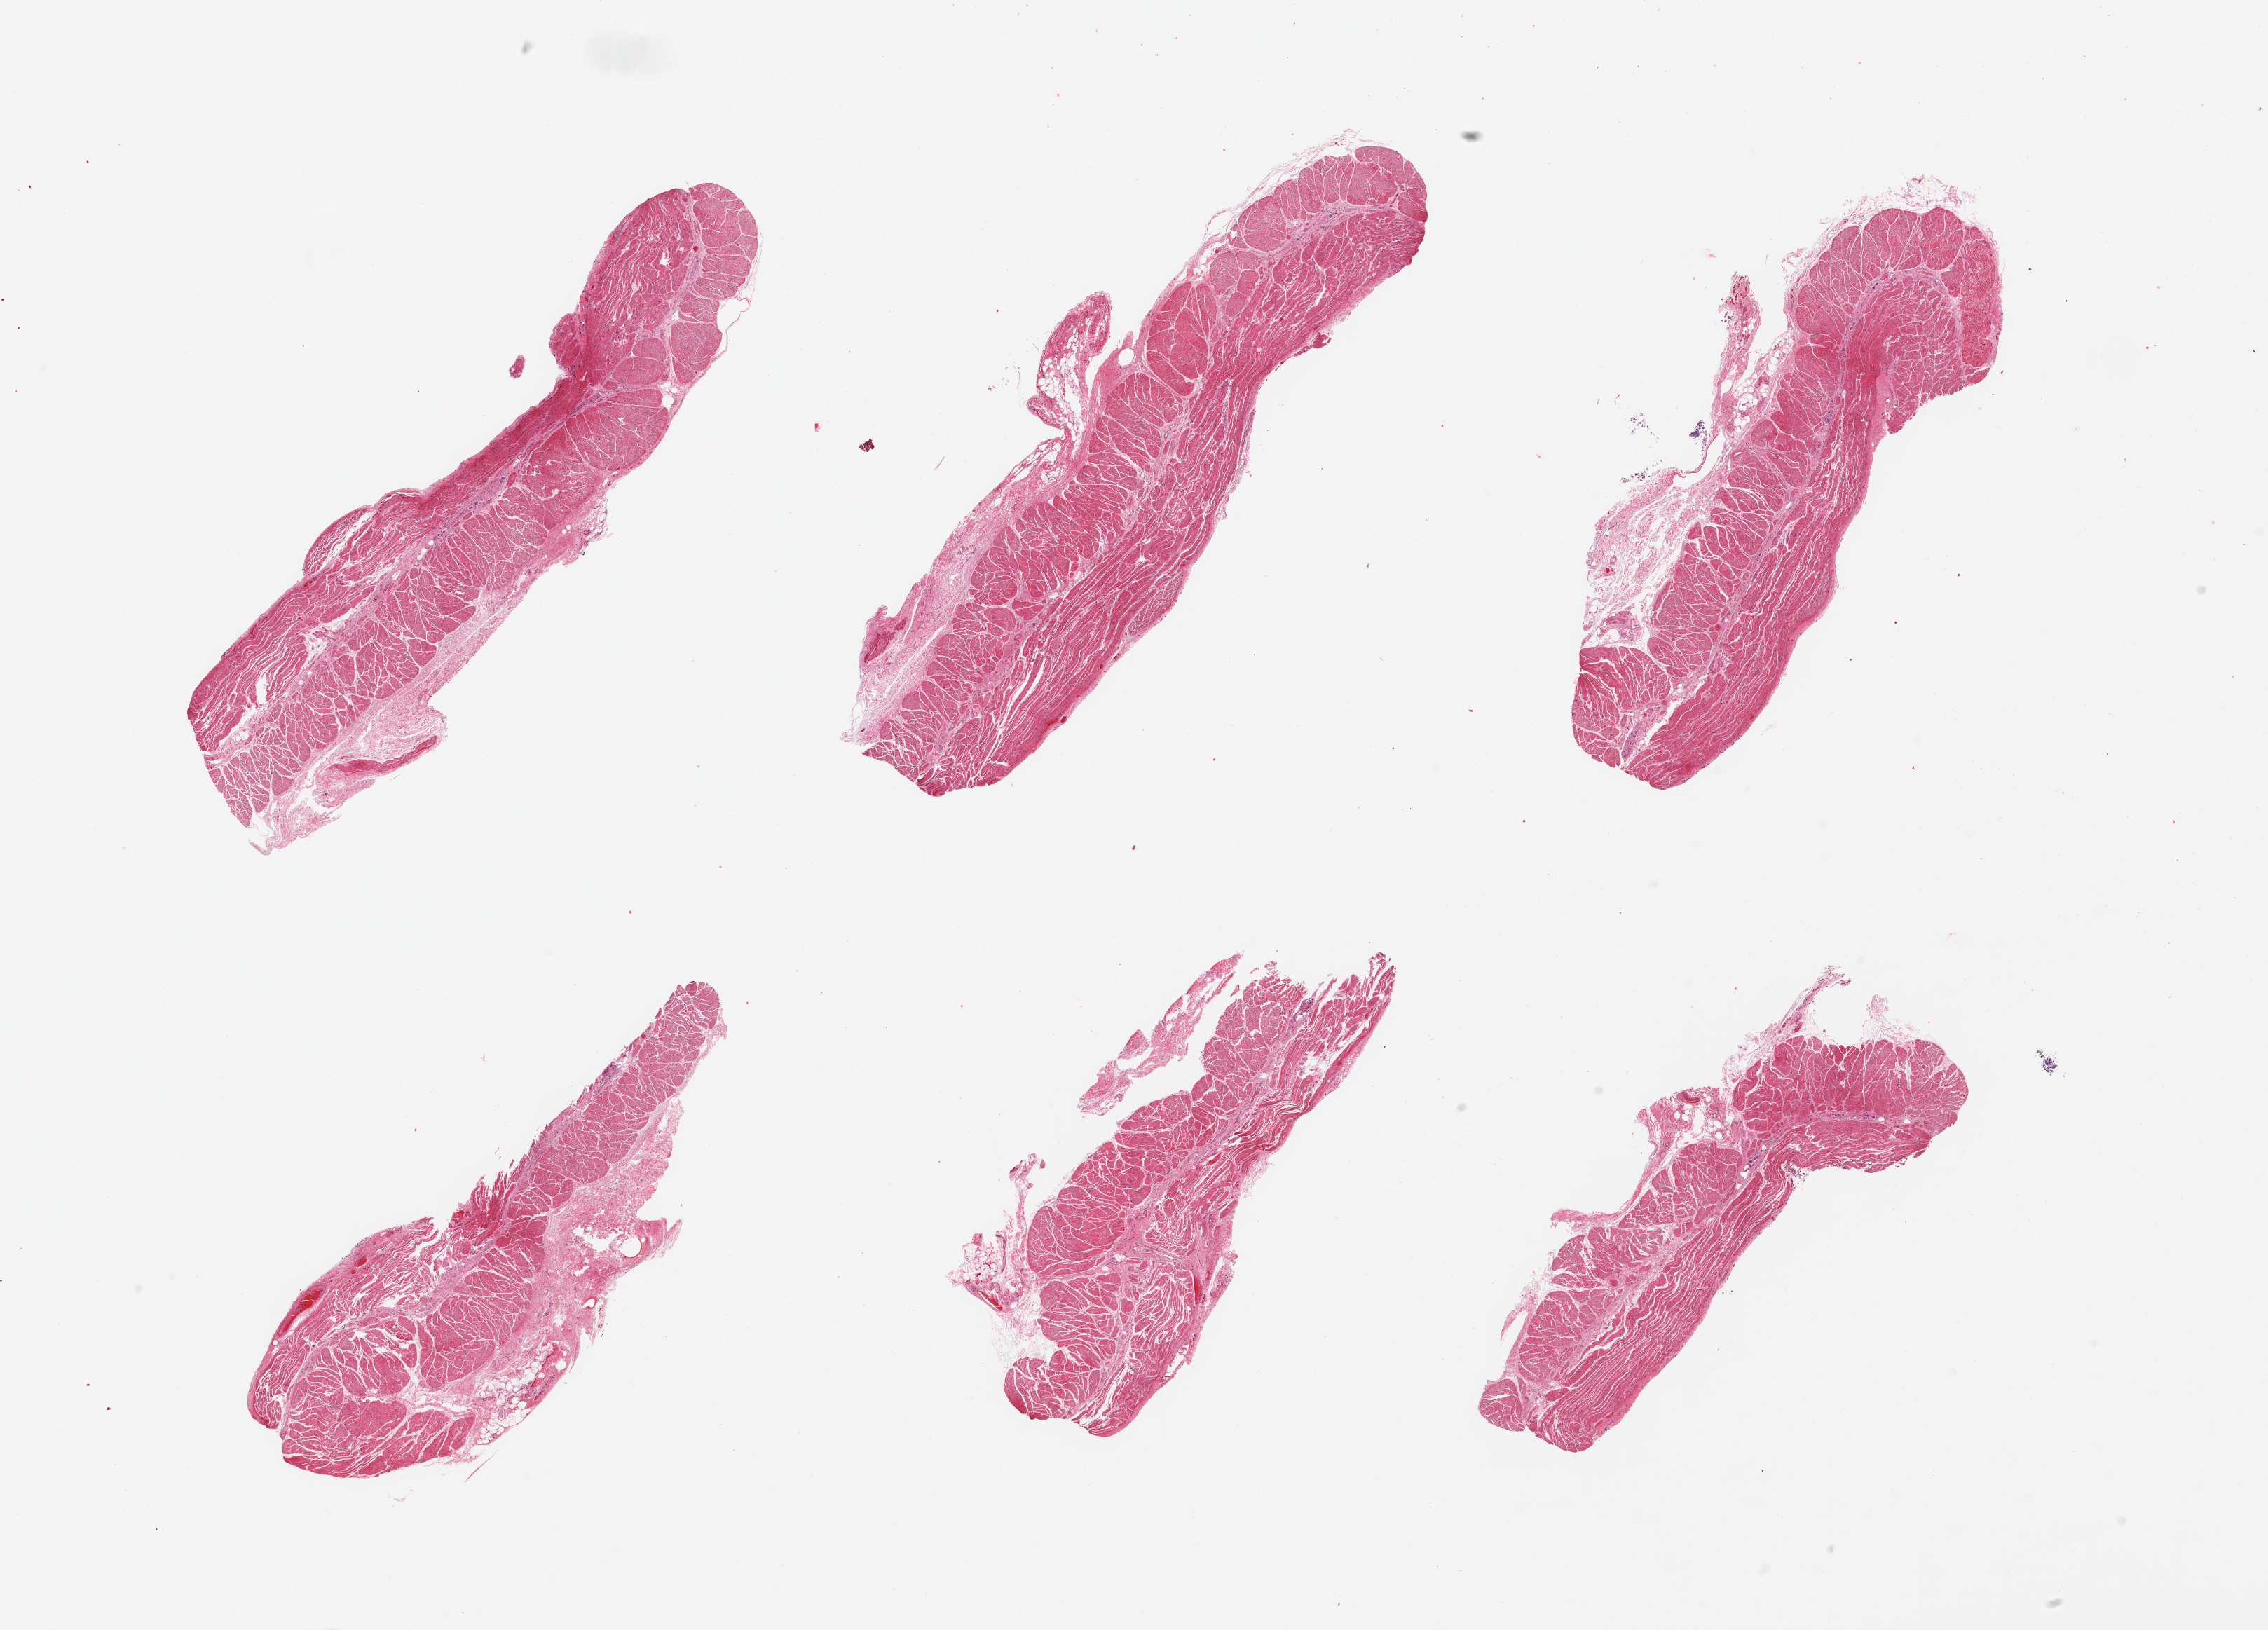
Digitized H&E-stained section, brightfield — low-resolution overview of the scanned area, about 25.6 x 18.4 mm, PAXgene-fixed, paraffin-embedded tissue, target tissue: gastroesophageal junction, tissue donor sample.
Reviewer comment on this tissue sample: 6 pieces, confirmed target muscularis, Myenteric nerve (ganglion) plexus unusually prominent.